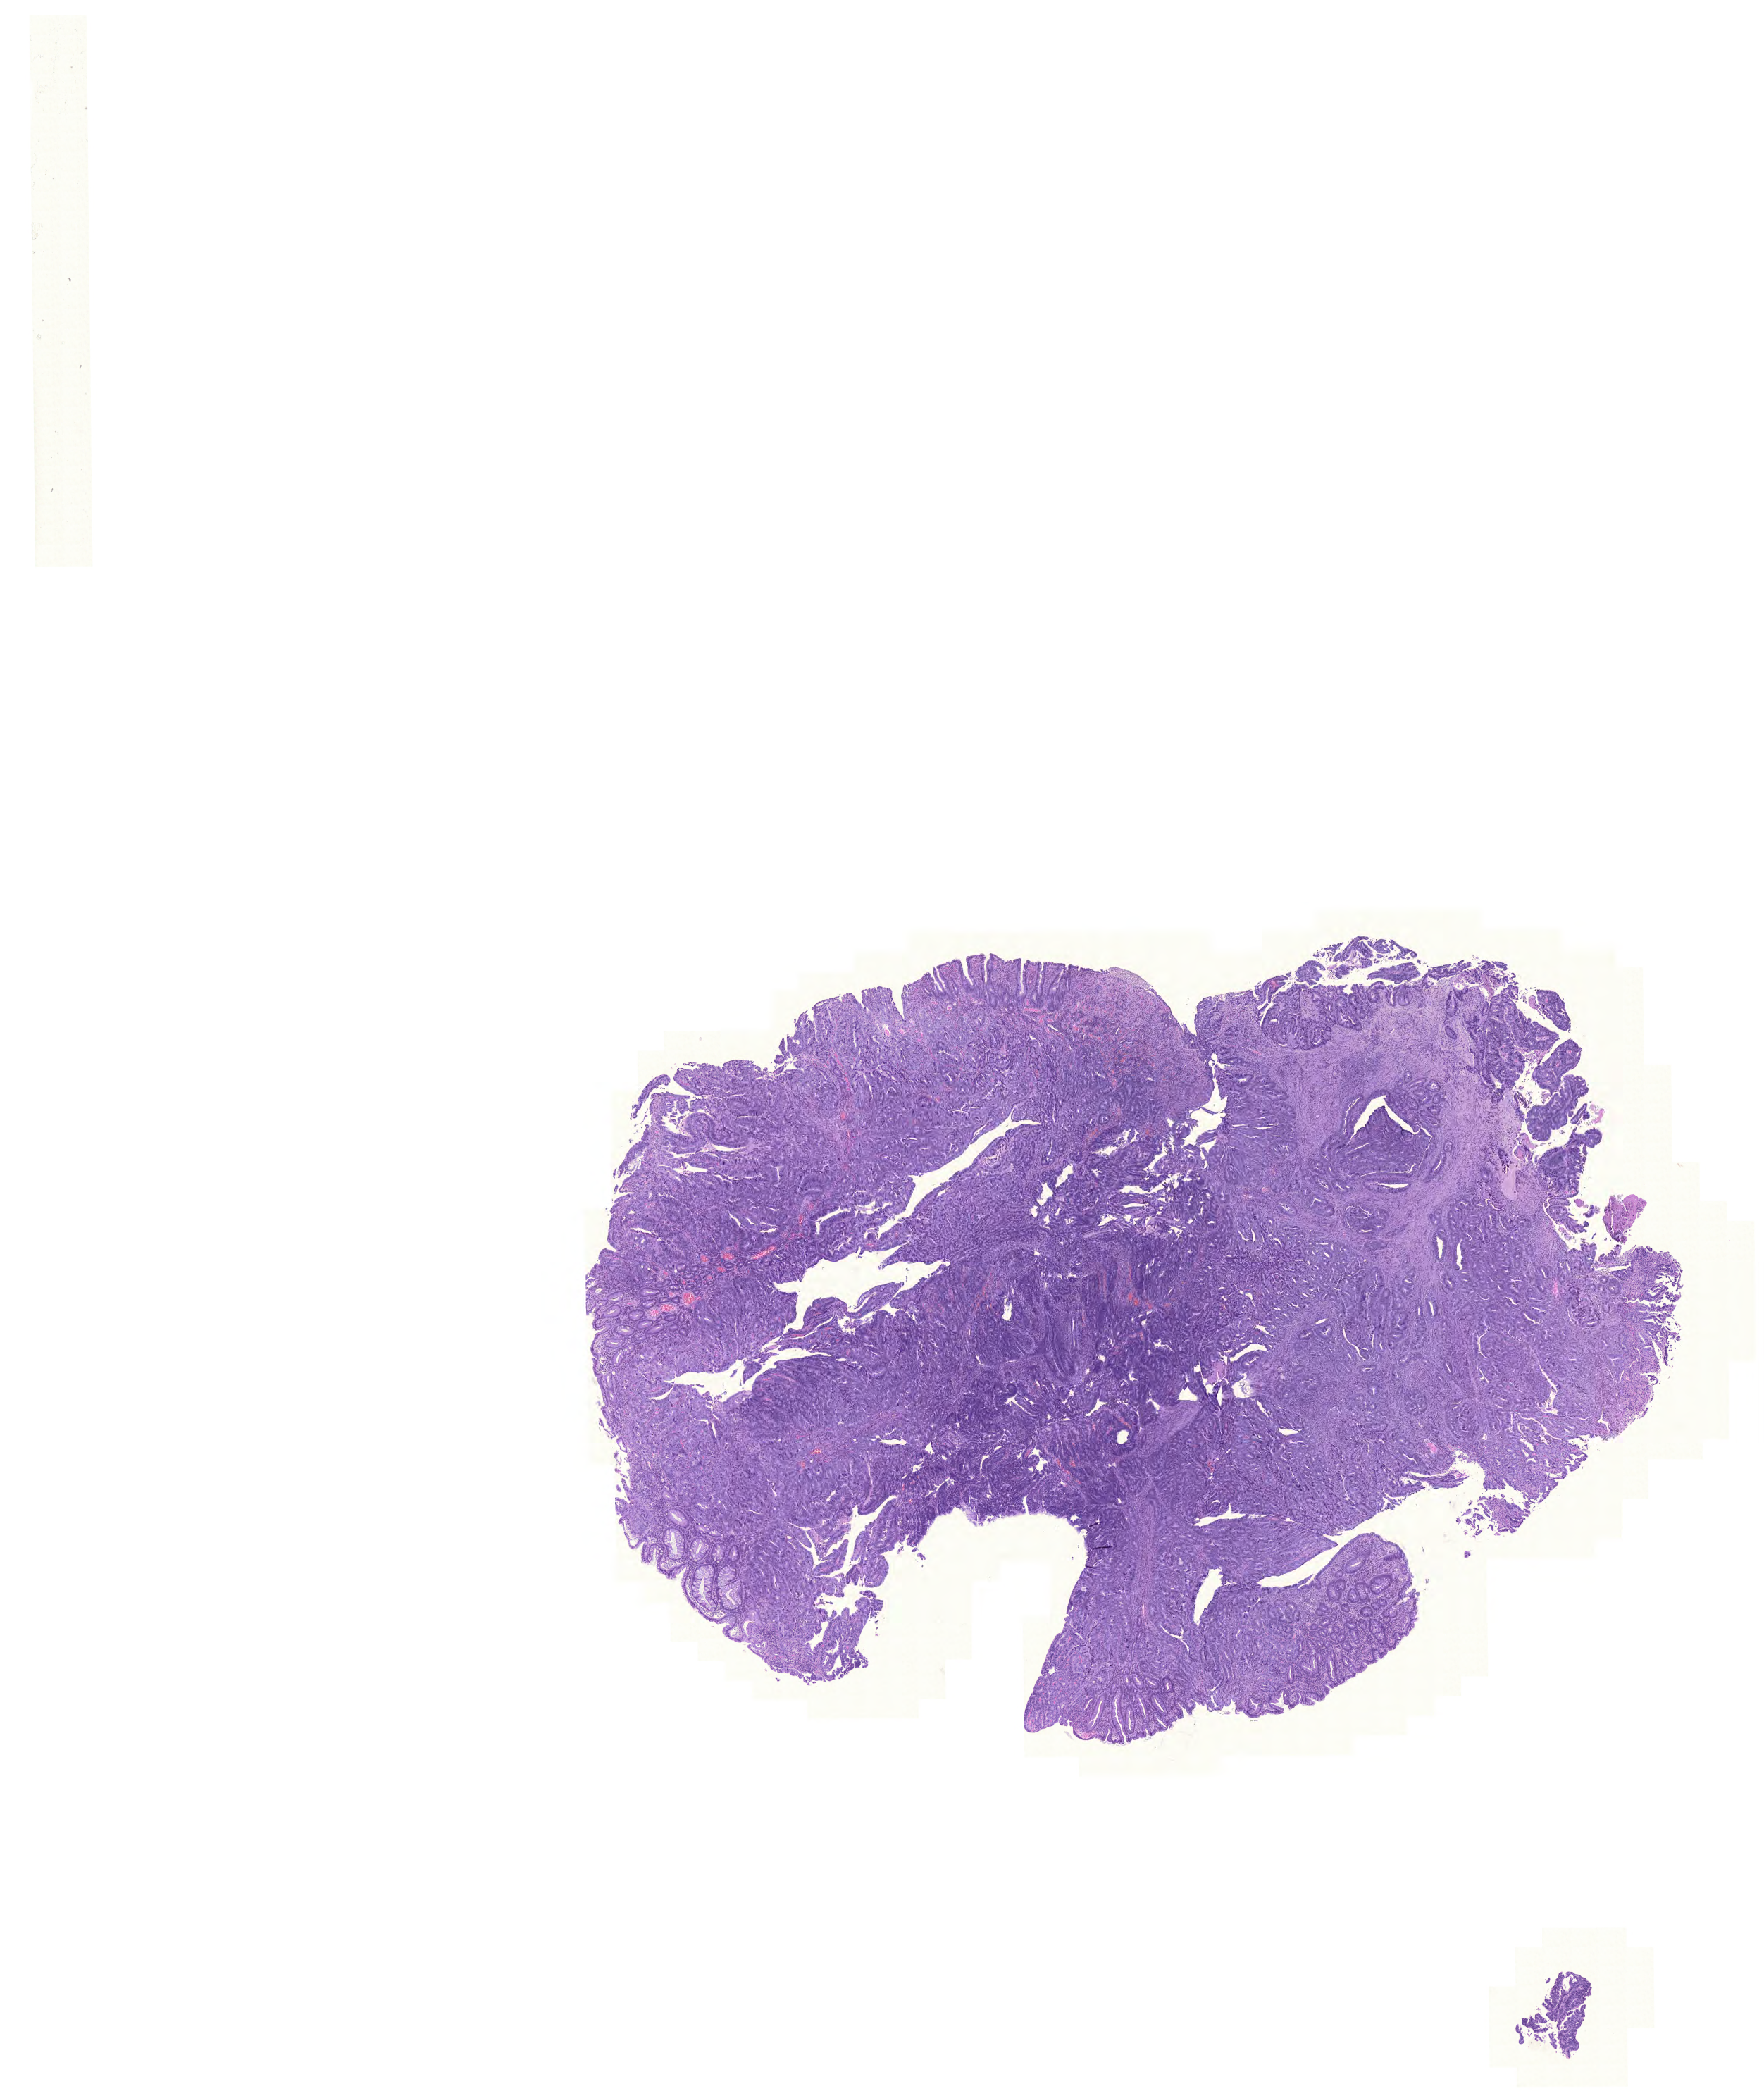
H&E-stained whole-slide image, whole scanned area (about 18.6 x 22.1 mm) shown as a low-resolution overview; FFPE section; rectum, primary tumour sample. Patient: male, age at initial diagnosis 63 years.
• pathologic diagnosis: Adenocarcinoma, NOS (rectosigmoid junction)
• lymph nodes positive (case pathology): 0 of 33 examined
• AJCC pathologic stage: I